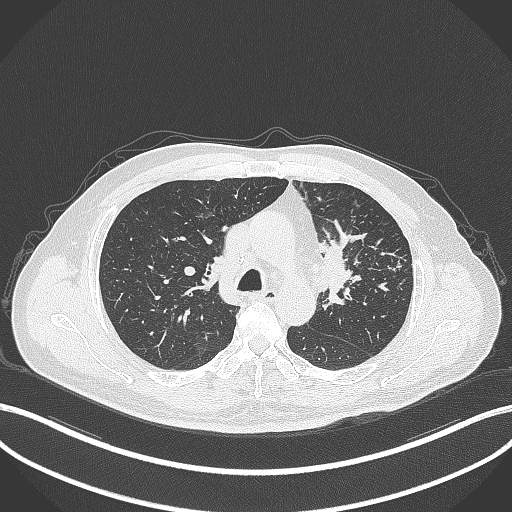
Chest CT, one axial slice. Slice 238 of 386 in the series (ordered by position). Lung window (W 1500 / L -600 HU). 1 mm slice thickness. 512 × 512 image matrix, field of view 400 × 400 mm. Male patient, age 69 years. Case-level facts recorded for this patient, not image findings: clinical TNM (as recorded): T2a N2 M0.
Structures marked on this image (rectangle marked by the reading radiologist):
- lung tumour (recorded histology: adenocarcinoma): box from (x=320, y=230) to (x=363, y=311) px